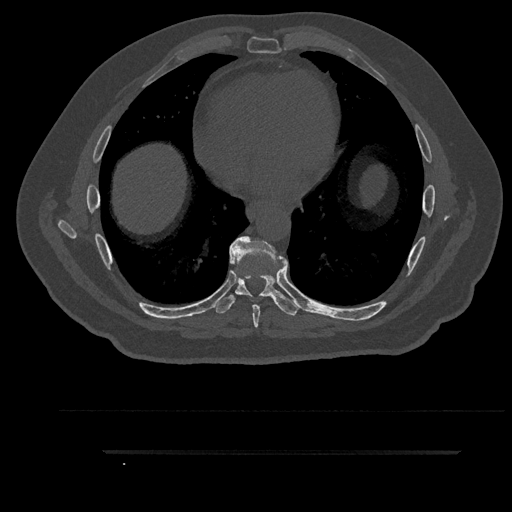
CT including the spine, one axial slice. Position 499 of 797 along the scan axis. Reconstruction kernel Br40s/3. Bone window (W 1800 / L 400 HU). 0.5 mm slice thickness. 512 × 512 image matrix, field of view 432 × 432 mm. Patient: male, 63 years. Case-level facts recorded for this patient, not image findings: primary cancer: renal.
Structures marked on this image (semi-automatically segmented with operator editing):
- T6 vertebra: bounding box (x1, y1, x2, y2) in pixels: (250, 295, 252, 297)
- T7 vertebra: (230, 236, 288, 328)
- T8 vertebra: (214, 248, 302, 316)